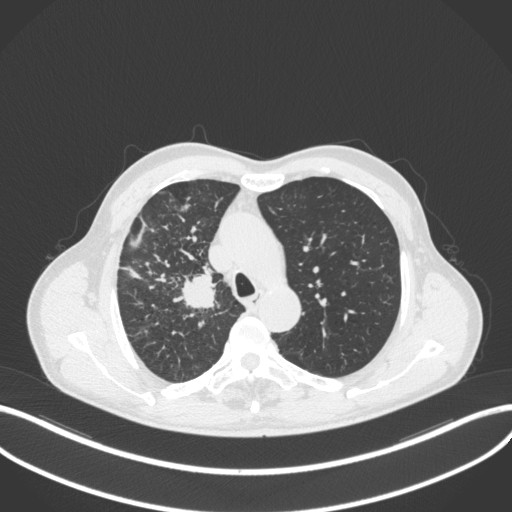
Chest CT, one axial slice; slice 350 of 490 in the series (ordered by position); lung window (W 1500 / L -600 HU); 1 mm slice thickness; 512 × 512 image matrix, field of view 400 × 400 mm. Patient: male, 69 years. From the clinical record (not read from this slice): clinical TNM (as recorded): T2a N0 M0.
Outlined on this slice (rectangle marked by the reading radiologist):
- lung tumour (recorded histology: adenocarcinoma): box from (x=178, y=268) to (x=223, y=315) px